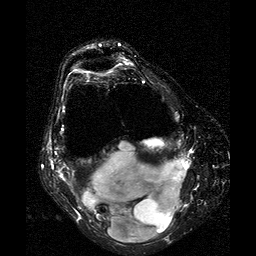
MRI of an extremity soft-tissue mass, one axial slice; position 13 of 25 along the scan axis; T2-weighted fat-saturated; 256 × 256 image matrix. Female patient. Case-level facts recorded for this patient, not image findings: histological type: liposarcoma; site of the primary tumour: right thigh.
Annotated regions visible in this slice (manually delineated by an expert):
- gross tumour volume (mass): bounding box <81,142,191,243> (left, top, right, bottom; pixels)